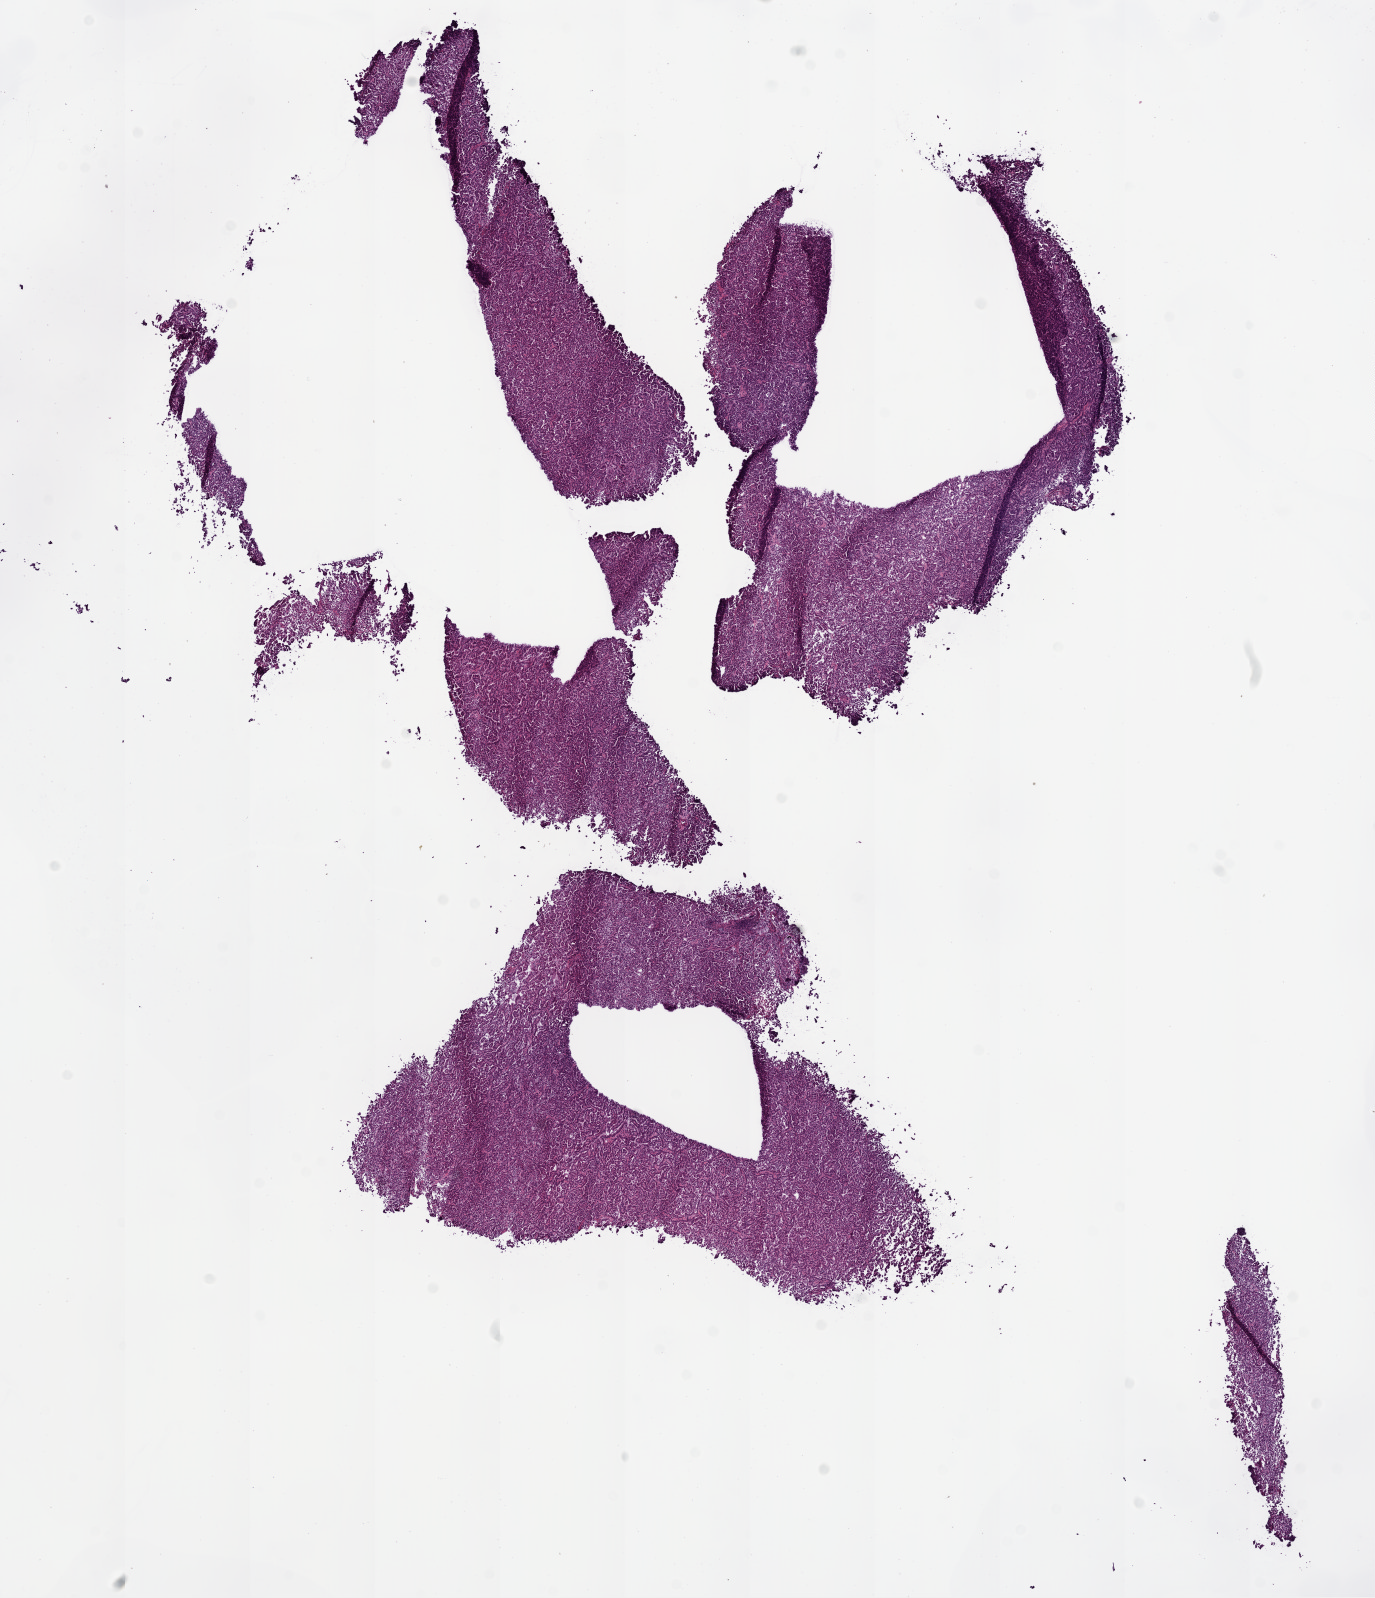
Digitized H&E tissue section (whole slide) — whole scanned area (about 11.0 x 12.8 mm) shown as a low-resolution overview. Frozen section from the bottom of the tissue portion. Primary tumour sample from the kidney. Male, age 51 years at initial diagnosis. Slide review estimates, as recorded: tumour cells 95%, tumour nuclei 85%, normal cells 0%, stromal cells 5%, necrosis 0%.
- AJCC pathologic stage: I
- histologic diagnosis: Papillary adenocarcinoma, NOS